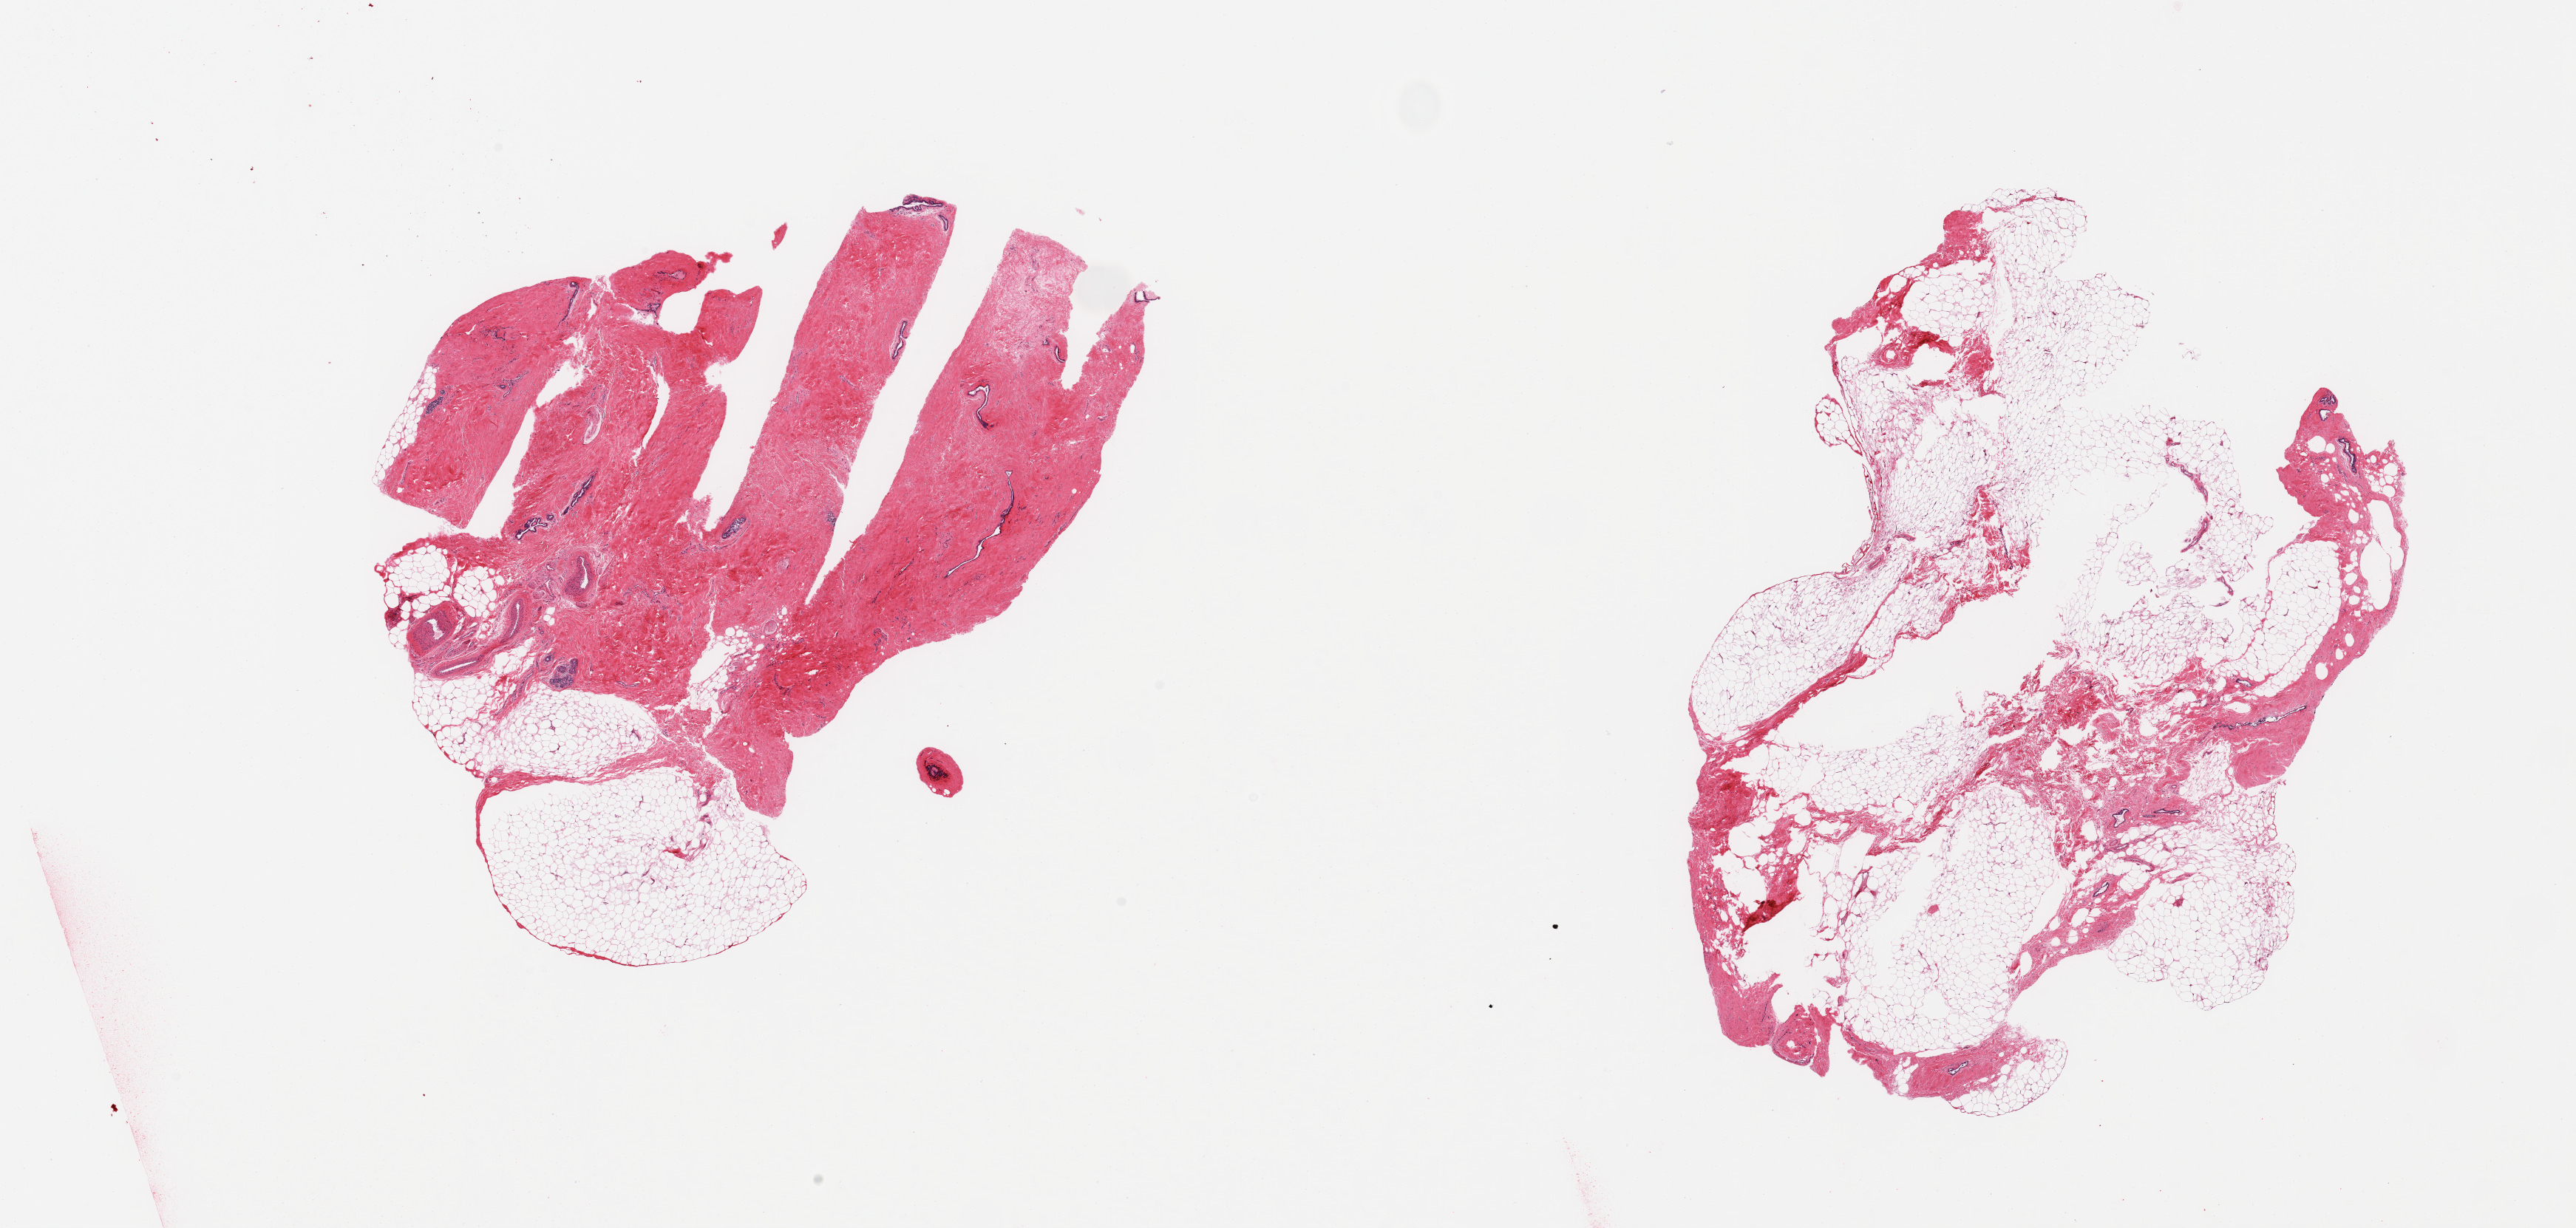
Digitized hematoxylin and eosin (H&E)-stained section, a low-resolution overview of the entire scanned area, about 27.6 x 13.1 mm (from a 20x scan). PAXgene-fixed paraffin-embedded (PFPE) section. Target tissue: breast. Tissue donor sample. Donor: male.
- reviewer comment on this tissue sample: 2 pieces; 1 is predominantly fat with smaller component of stroma/ducts, 2nd is mostly dense stroma with scattered ducts and ~20% fat